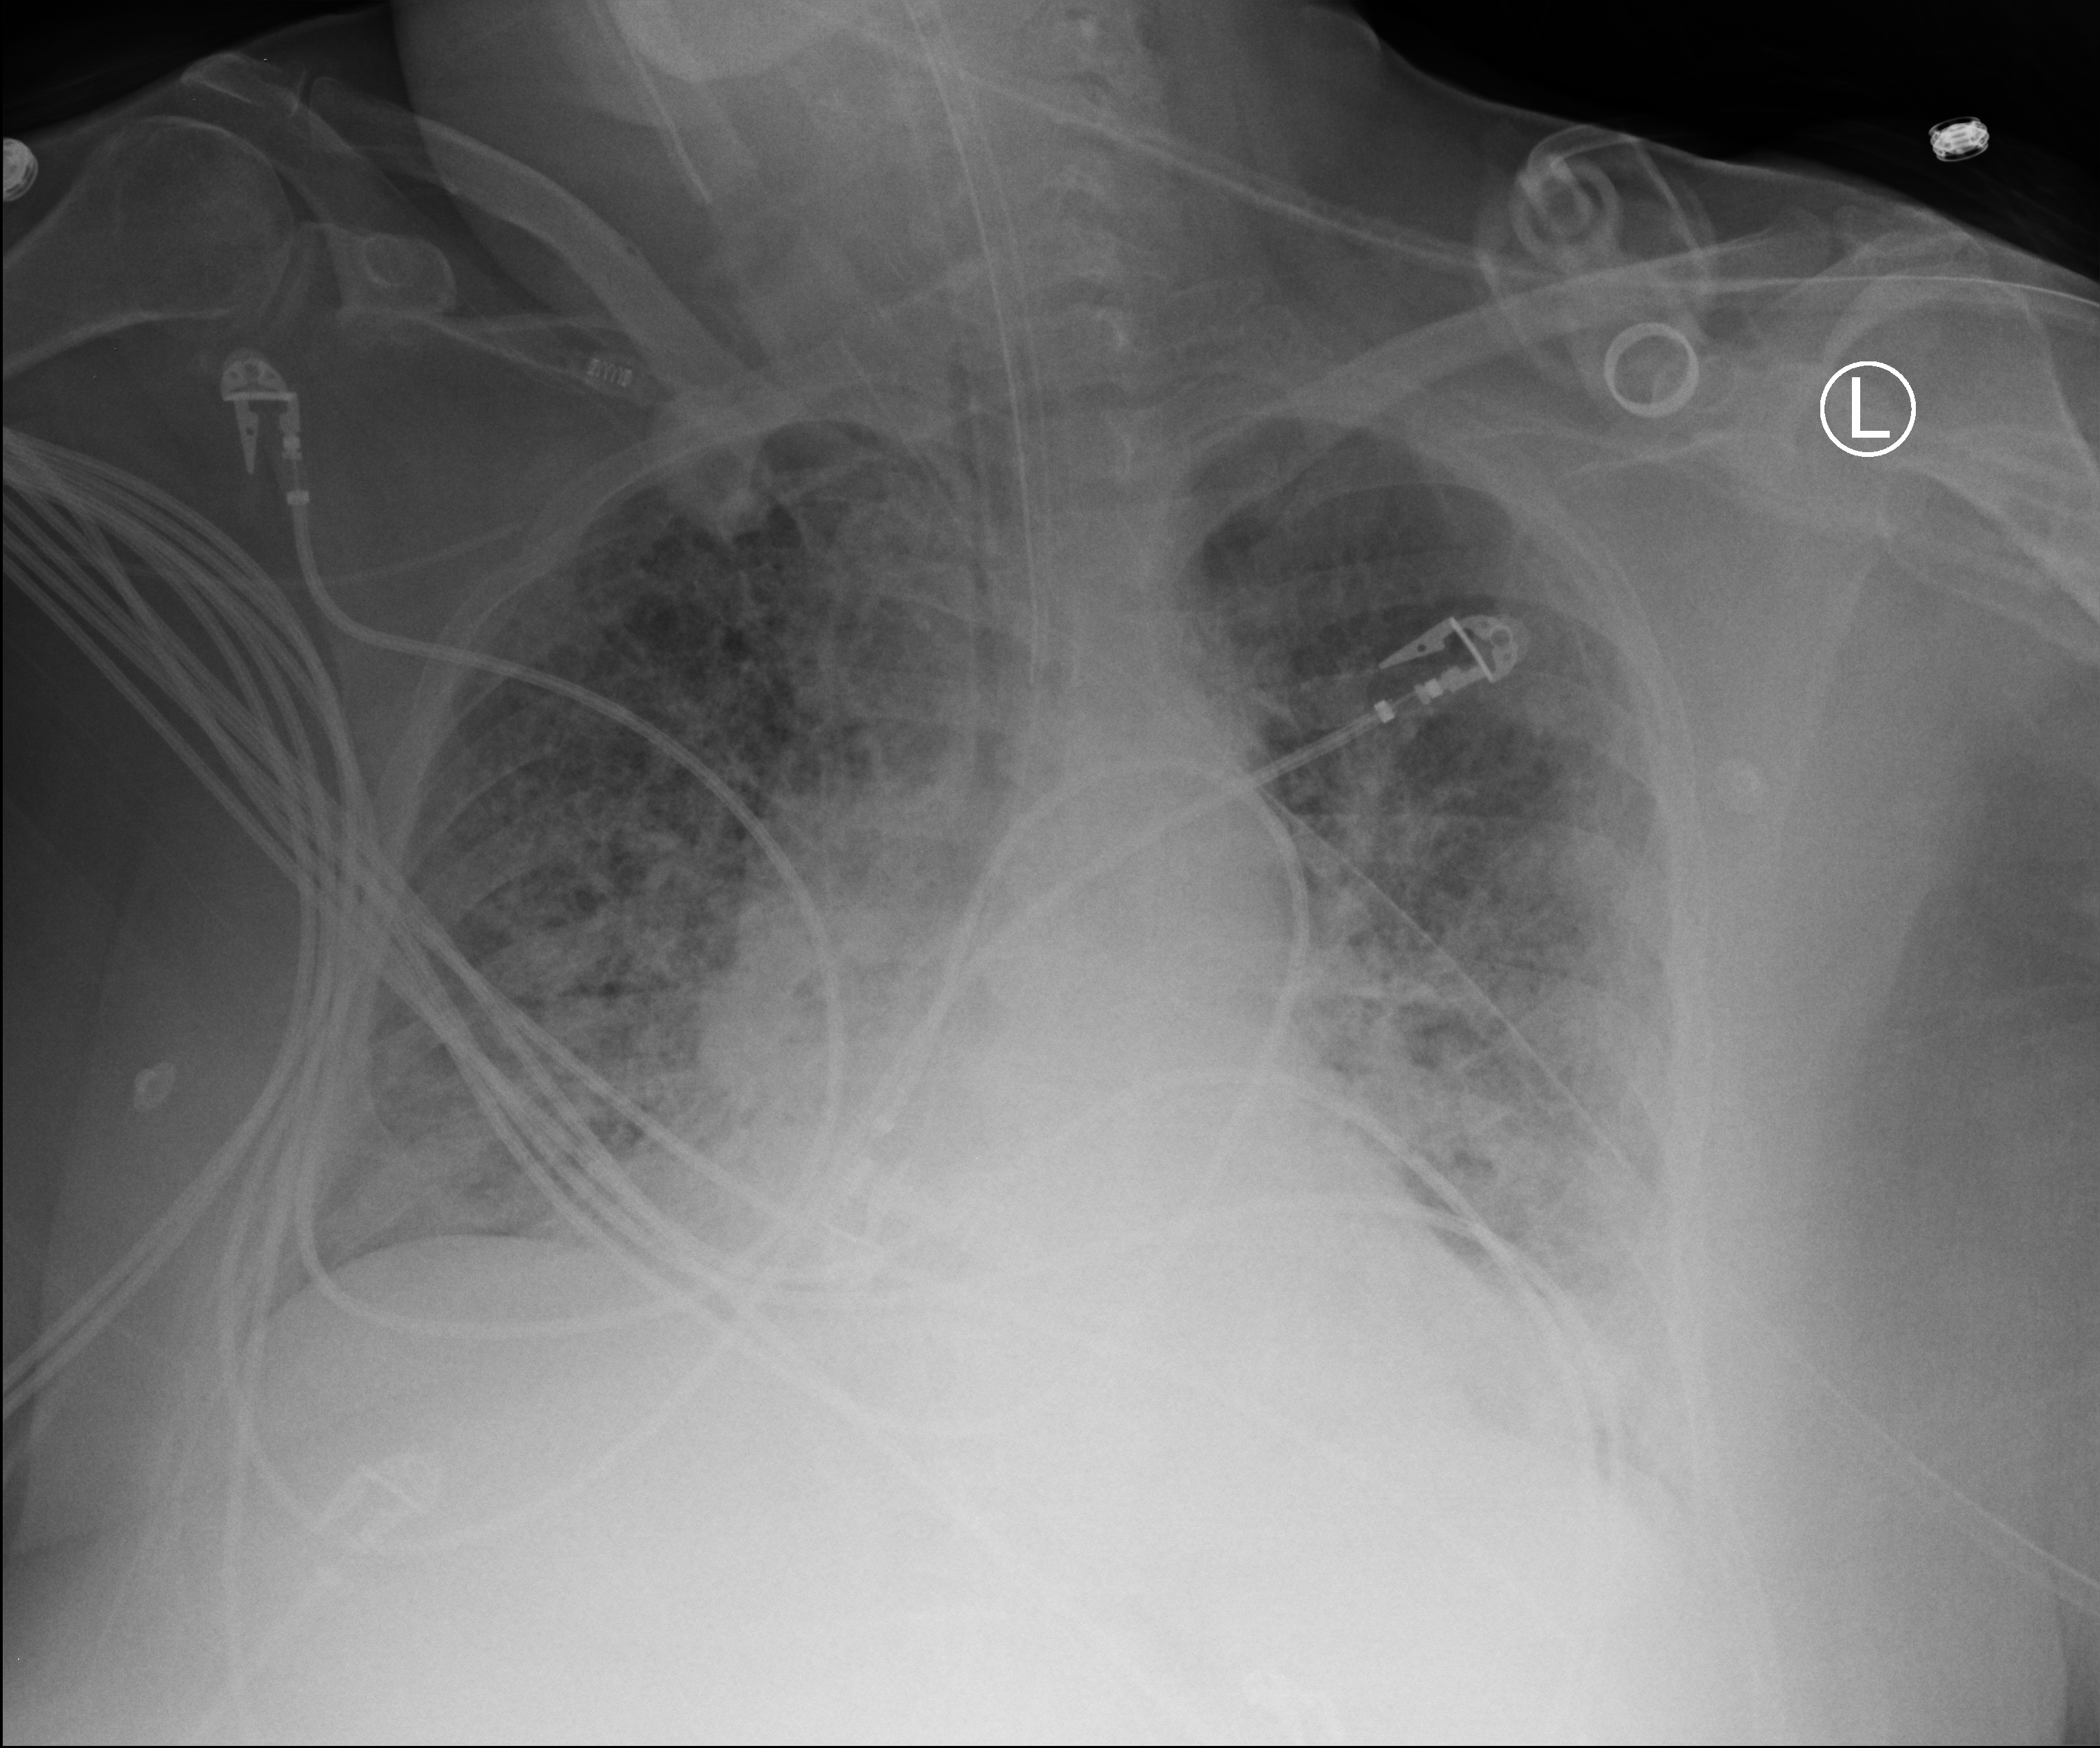
Bedside chest radiograph (computed radiography), anteroposterior (AP) projection. Female patient hospitalised with COVID-19, age 60–74 years.
Admission-level facts for this patient (not findings on this image; timing relative to this image not recorded): smoking status (admission record): former; length of hospital stay: 28 days.